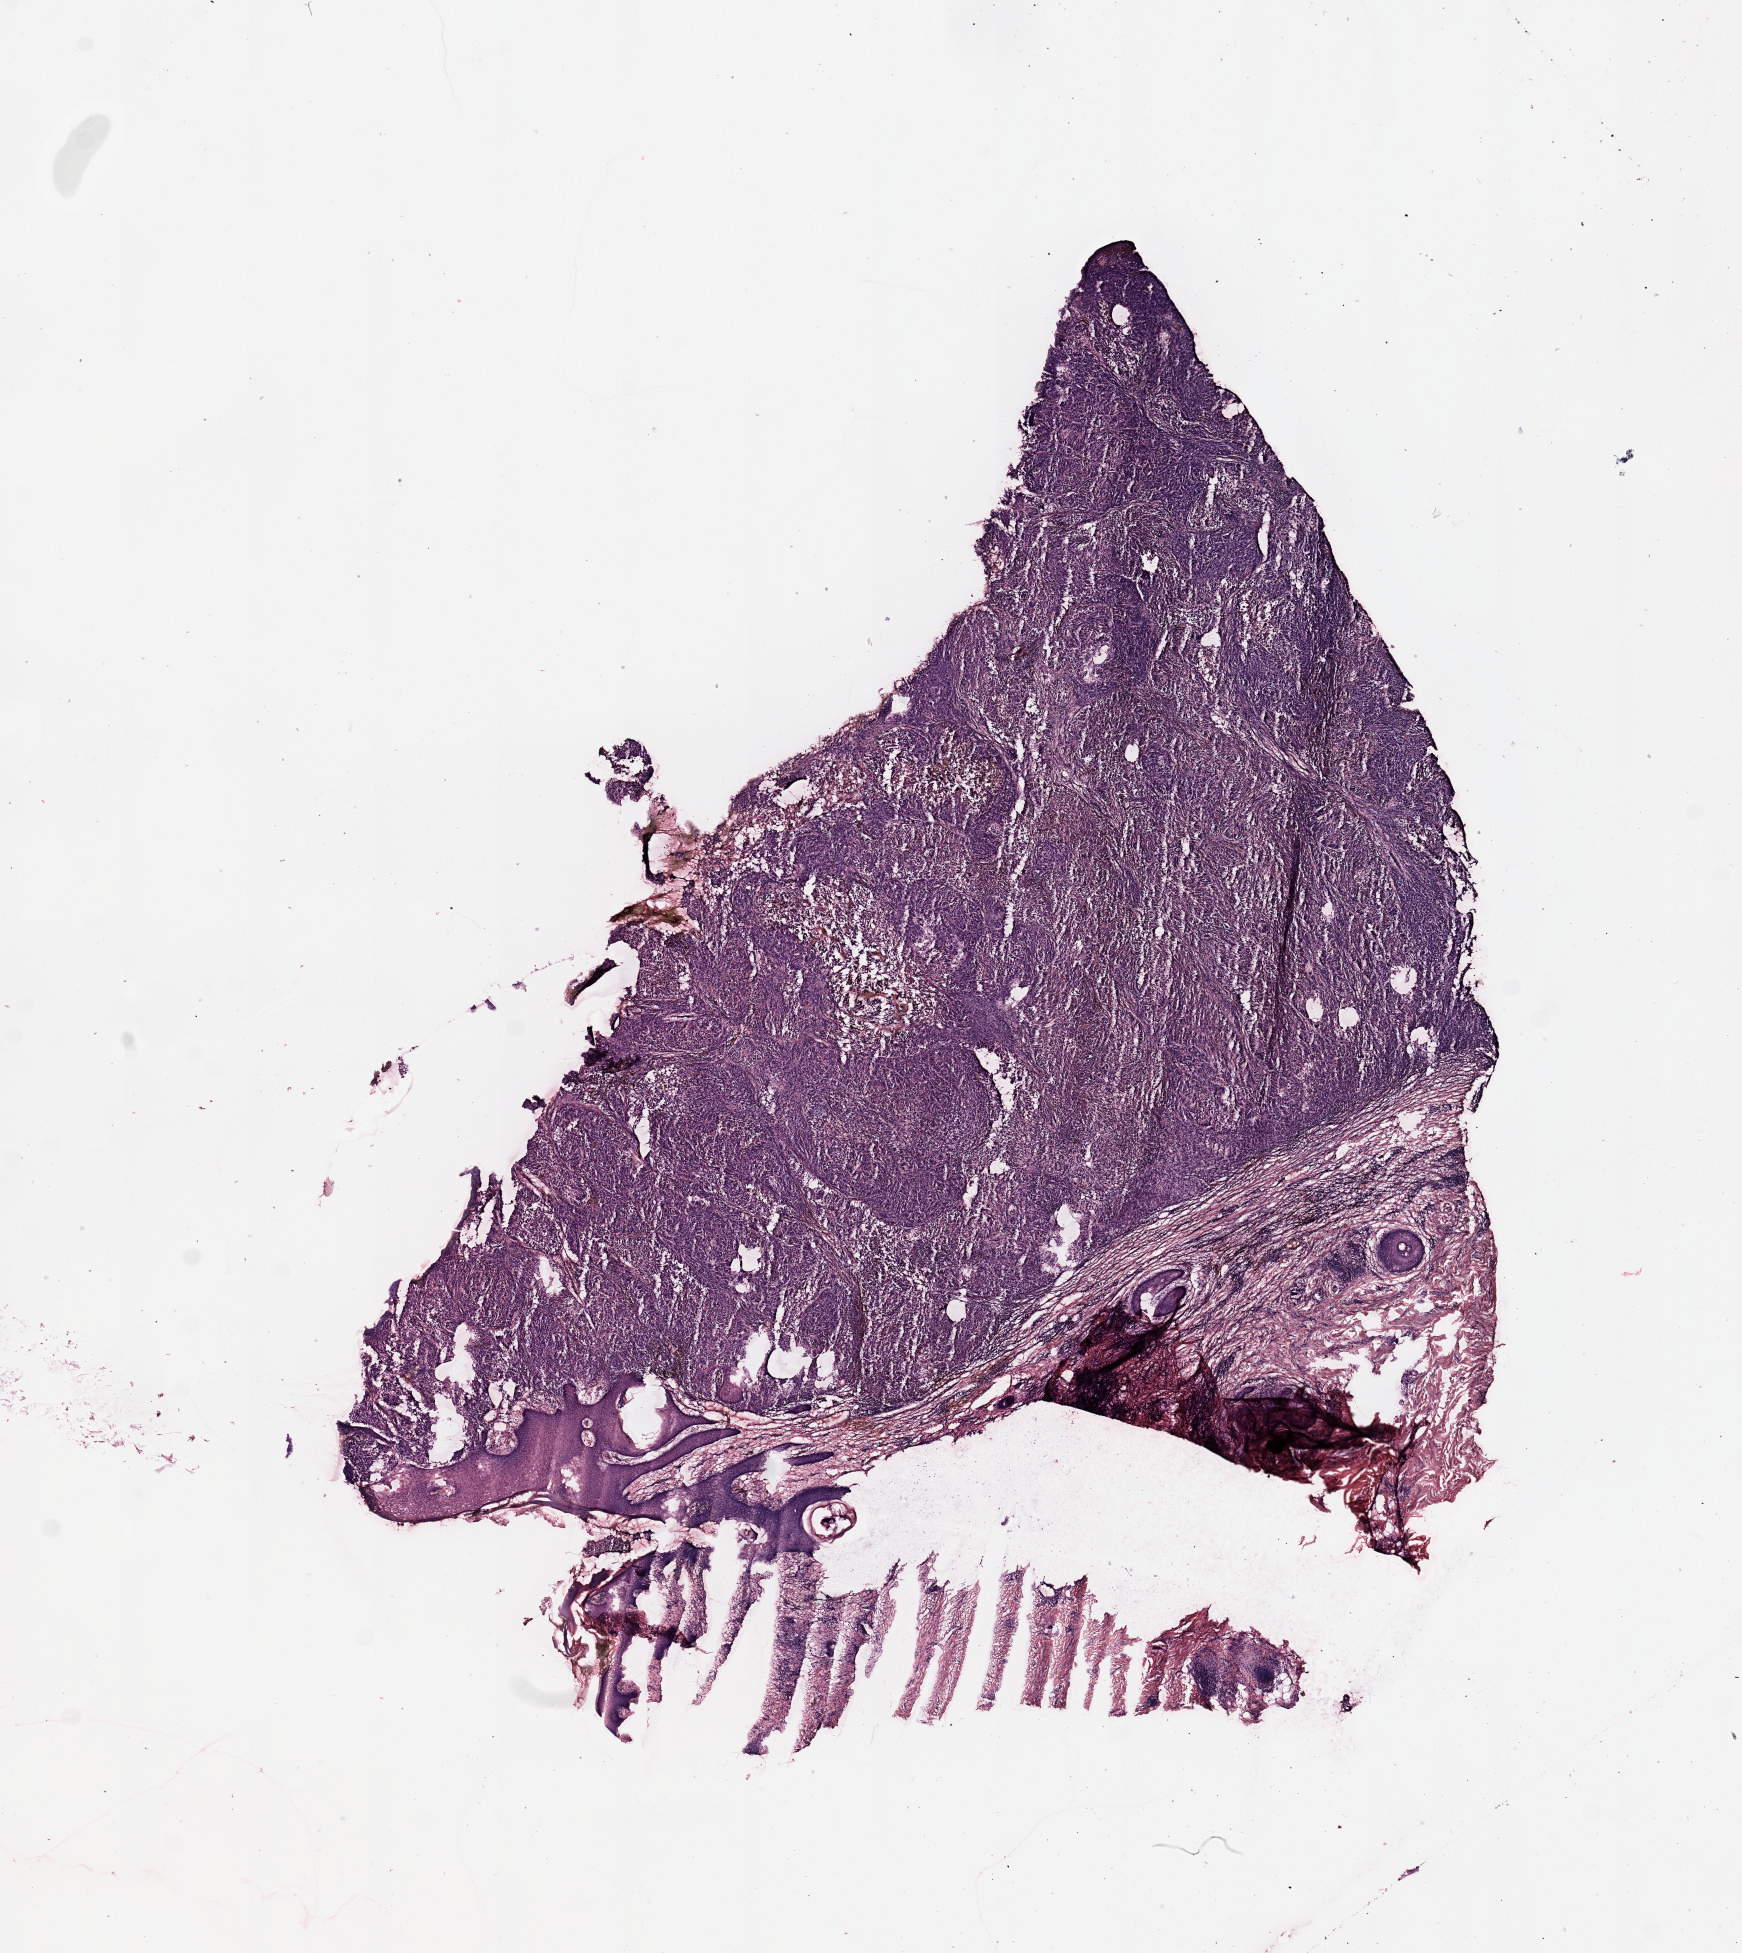
H&E whole-slide image — a low-resolution overview of the entire scanned area, about 13.8 x 15.5 mm, melanoma tumour tissue; sampled site not recorded. Patient: male, age 61 years.
* patient diagnosis (cohort enrolment): cutaneous melanoma (skin)
* primary tumour site (as recorded): trunk